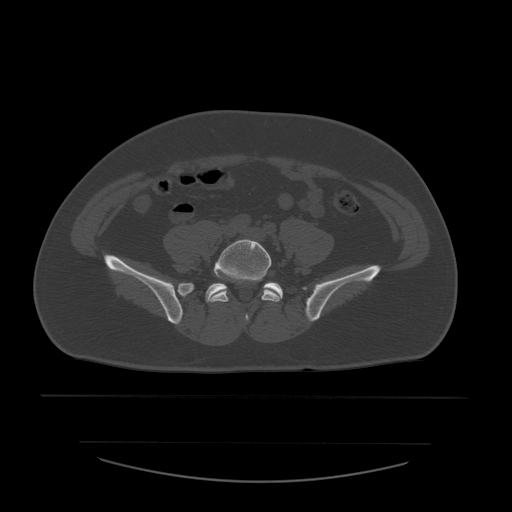
CT including the spine, one axial slice. Slice 113 of 532 in the series (ordered by position). 120 kVp. Bone window (W 1800 / L 400 HU). 1.25 mm slice thickness. 512 × 512 image matrix. Patient age 44 years. Case-level facts recorded for this patient, not image findings: primary cancer: soft tissue sarcoma.
Structures marked on this image (semi-automatically segmented with operator editing):
- L5 vertebra: bounding box <208,239,283,321> (left, top, right, bottom; pixels)